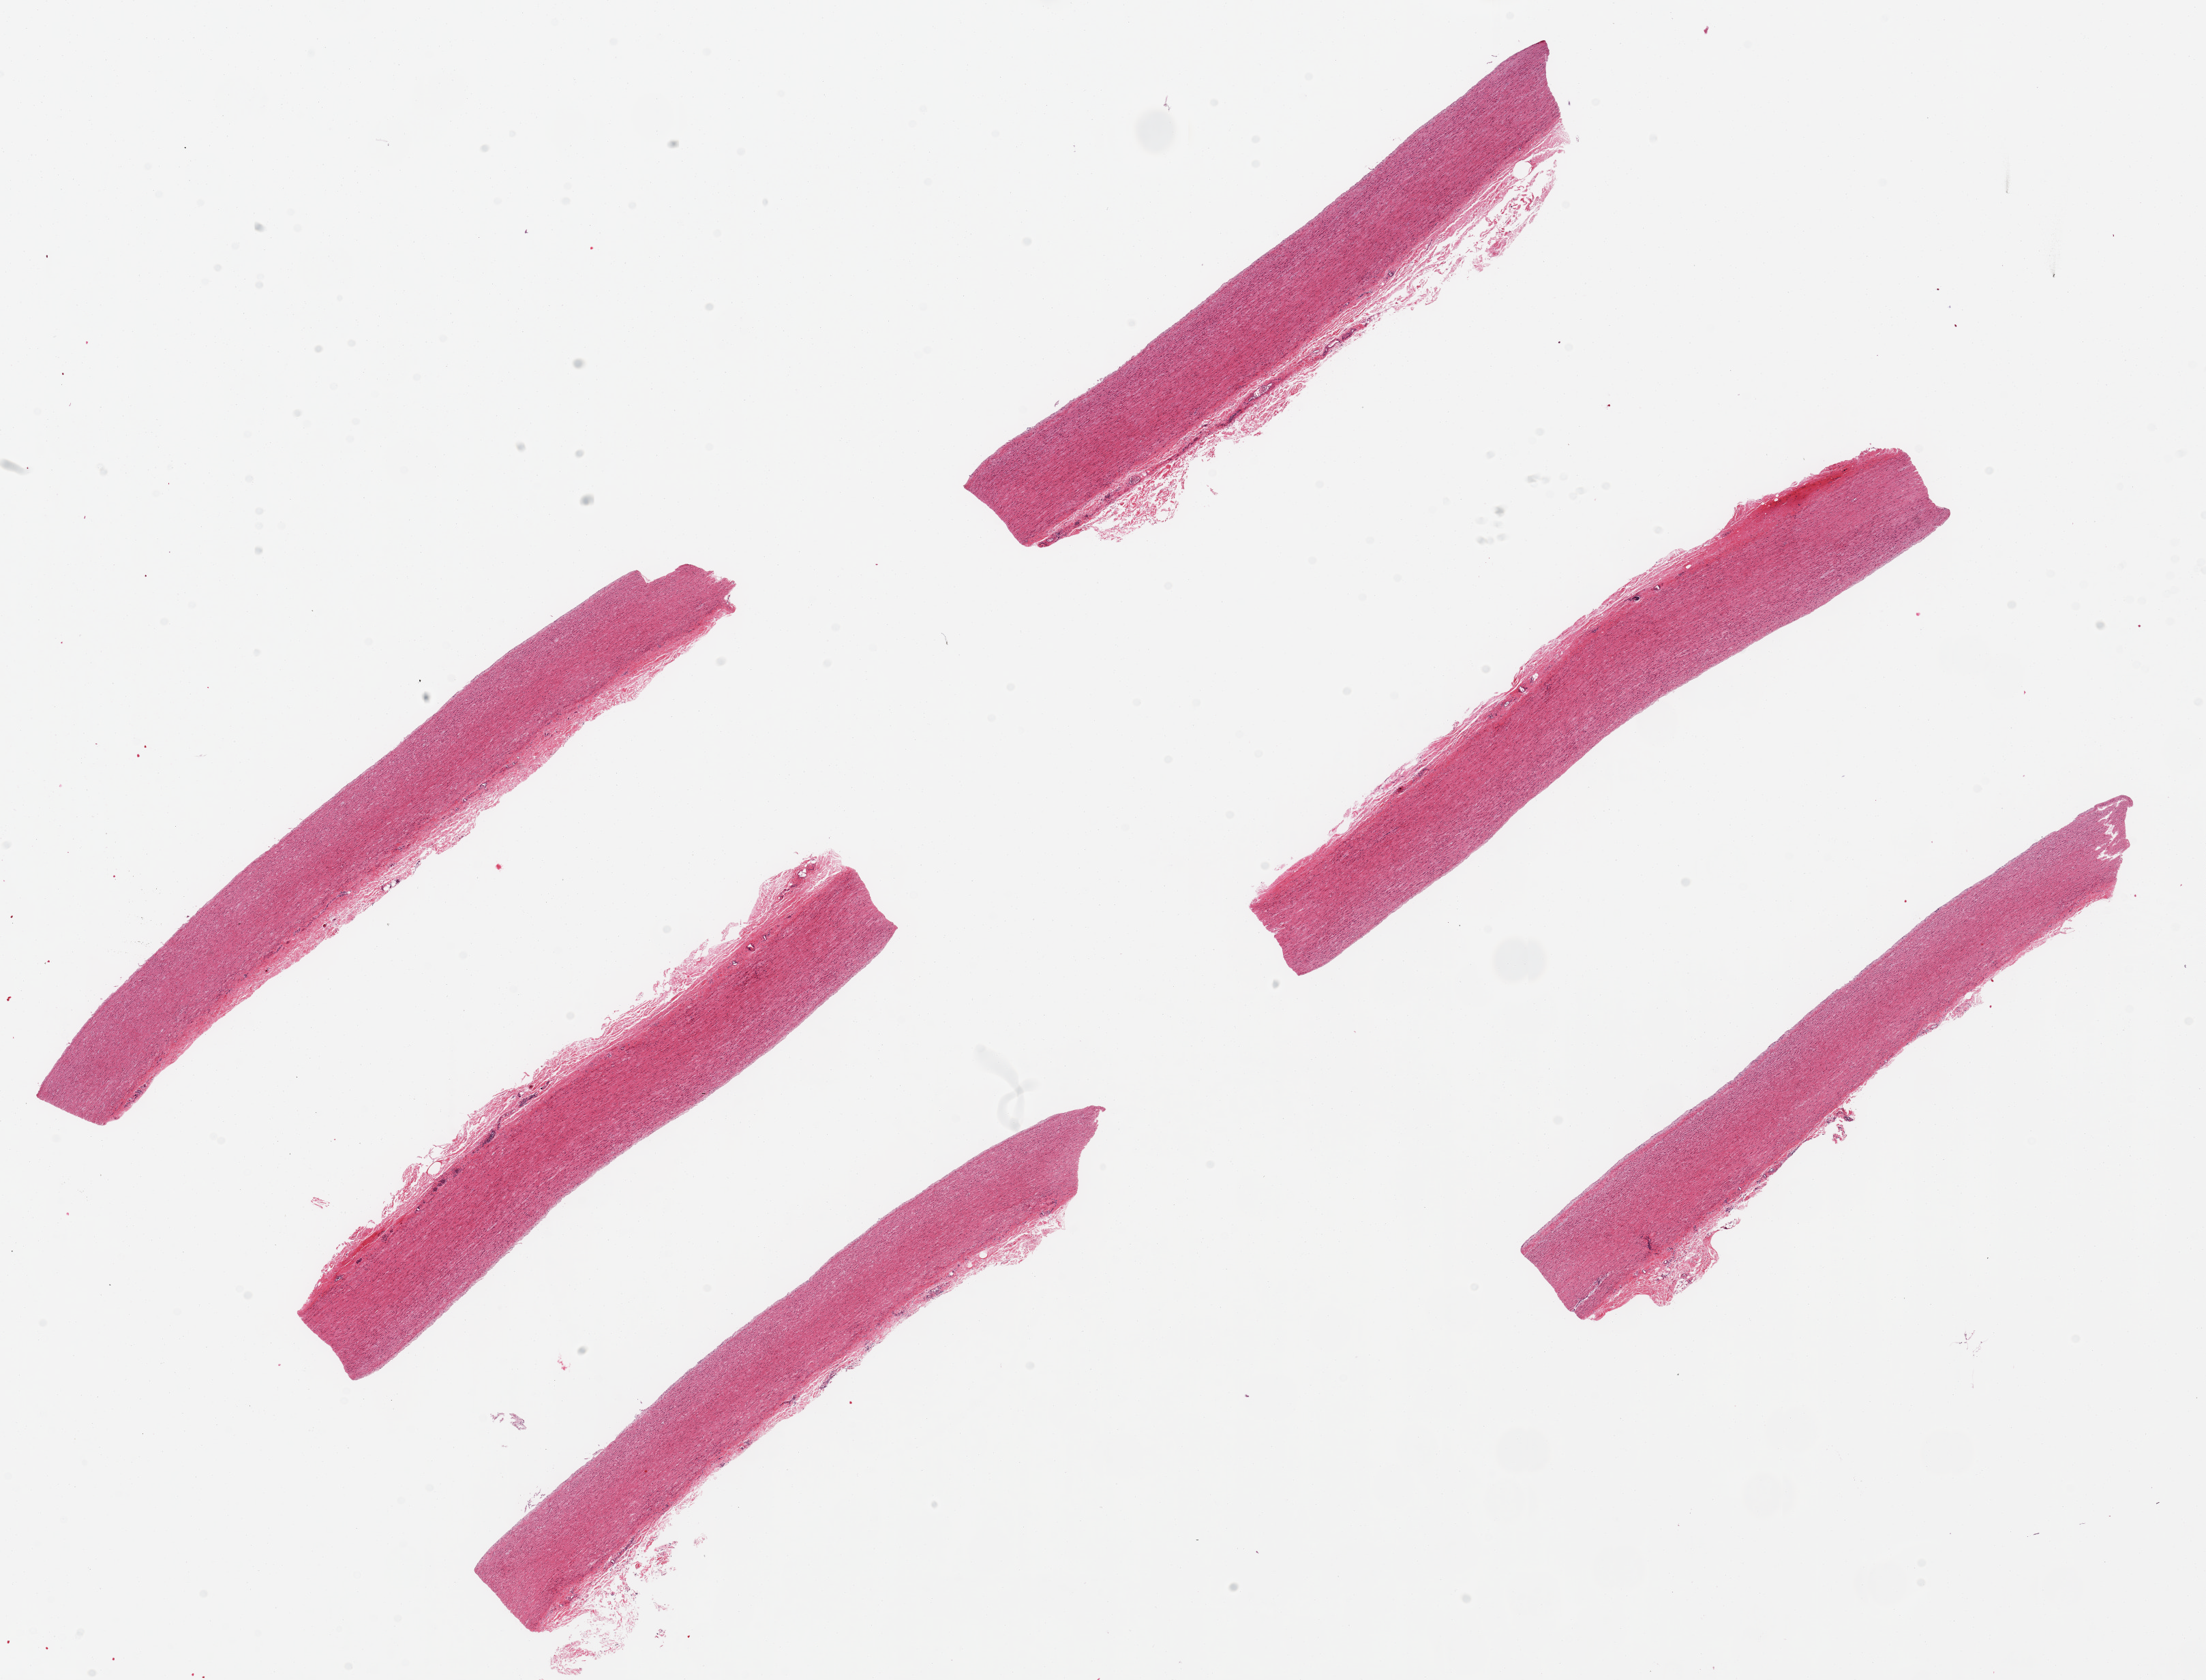
Digitized hematoxylin and eosin (H&E)-stained section — a low-resolution overview of the entire scanned area, about 25.6 x 19.5 mm (from a 20x scan), PAXgene-fixed, paraffin-embedded tissue, section of aorta (target tissue), donor tissue sample. Donor: female.
Reviewer comment on this tissue sample: 6 pieces, ~9x1 mm; normal aorta.